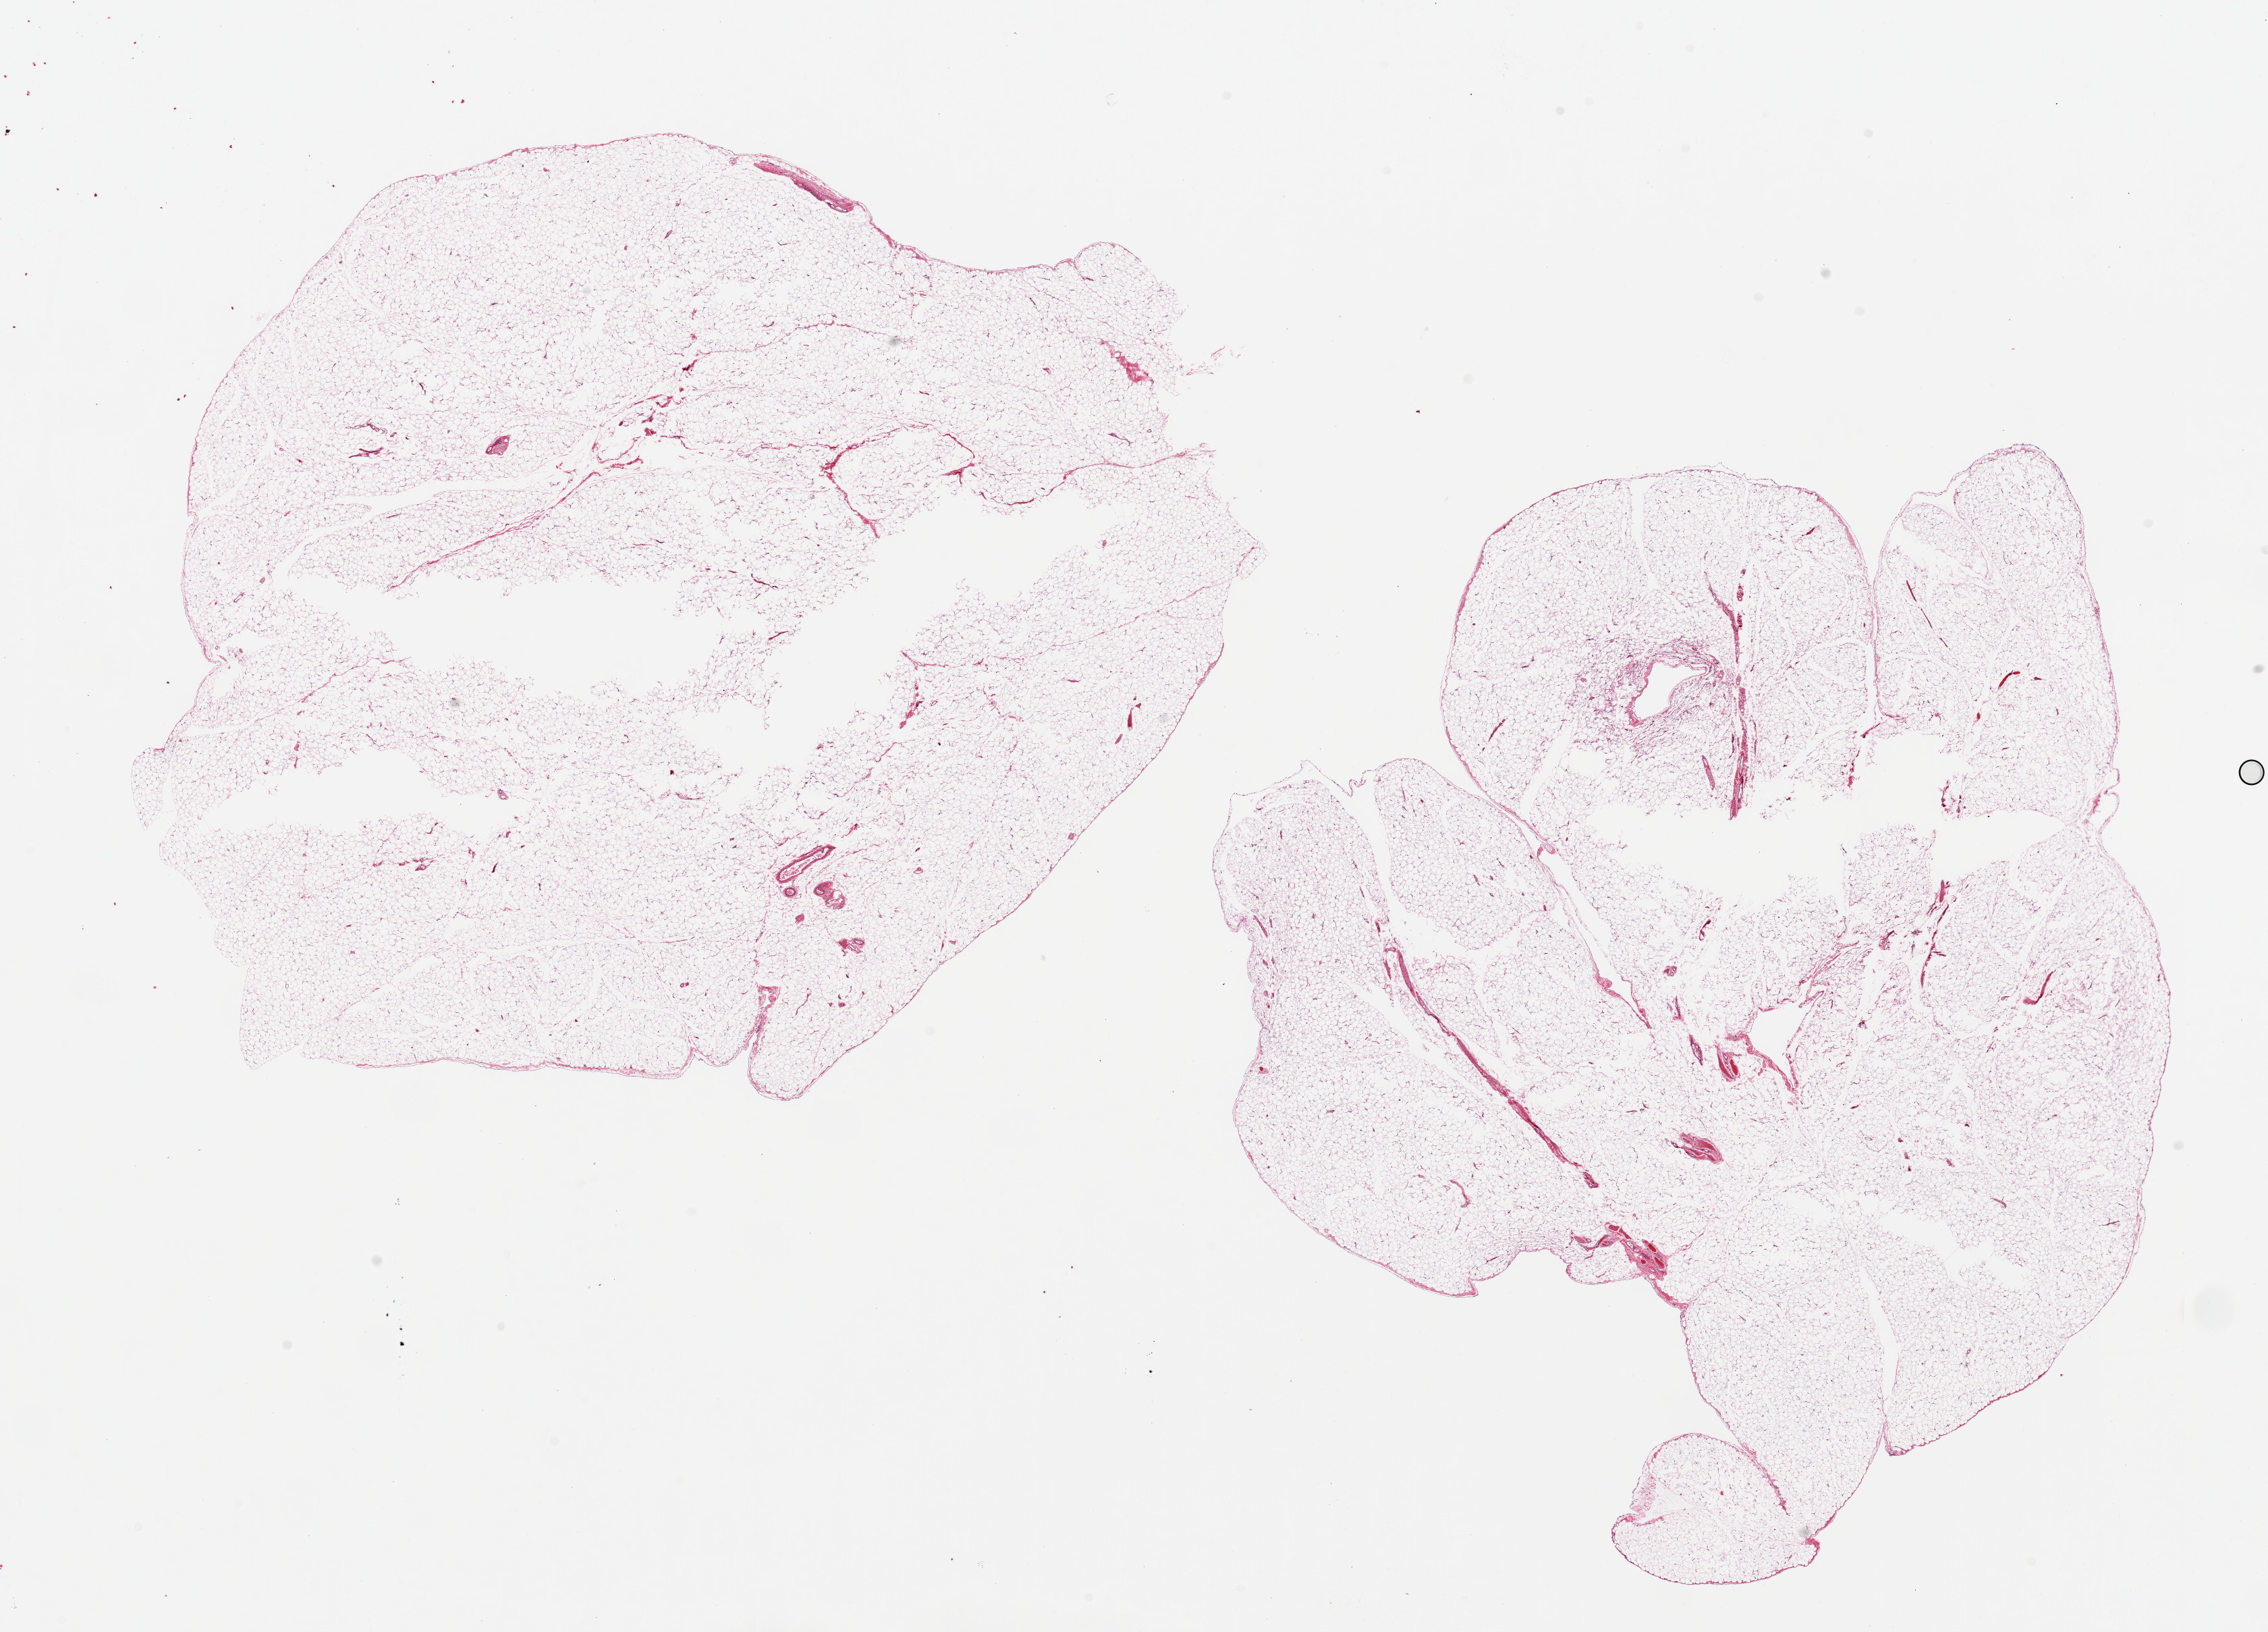
Whole-slide image, haematoxylin and eosin stain, low-resolution overview of the scanned area, about 26.6 x 19.1 mm (acquisition: 20x scan); PAXgene-fixed paraffin-embedded (PFPE) section; section of omentum (target tissue); donor tissue sample.
Review note (as recorded): 2 pieces ~12x11mm.